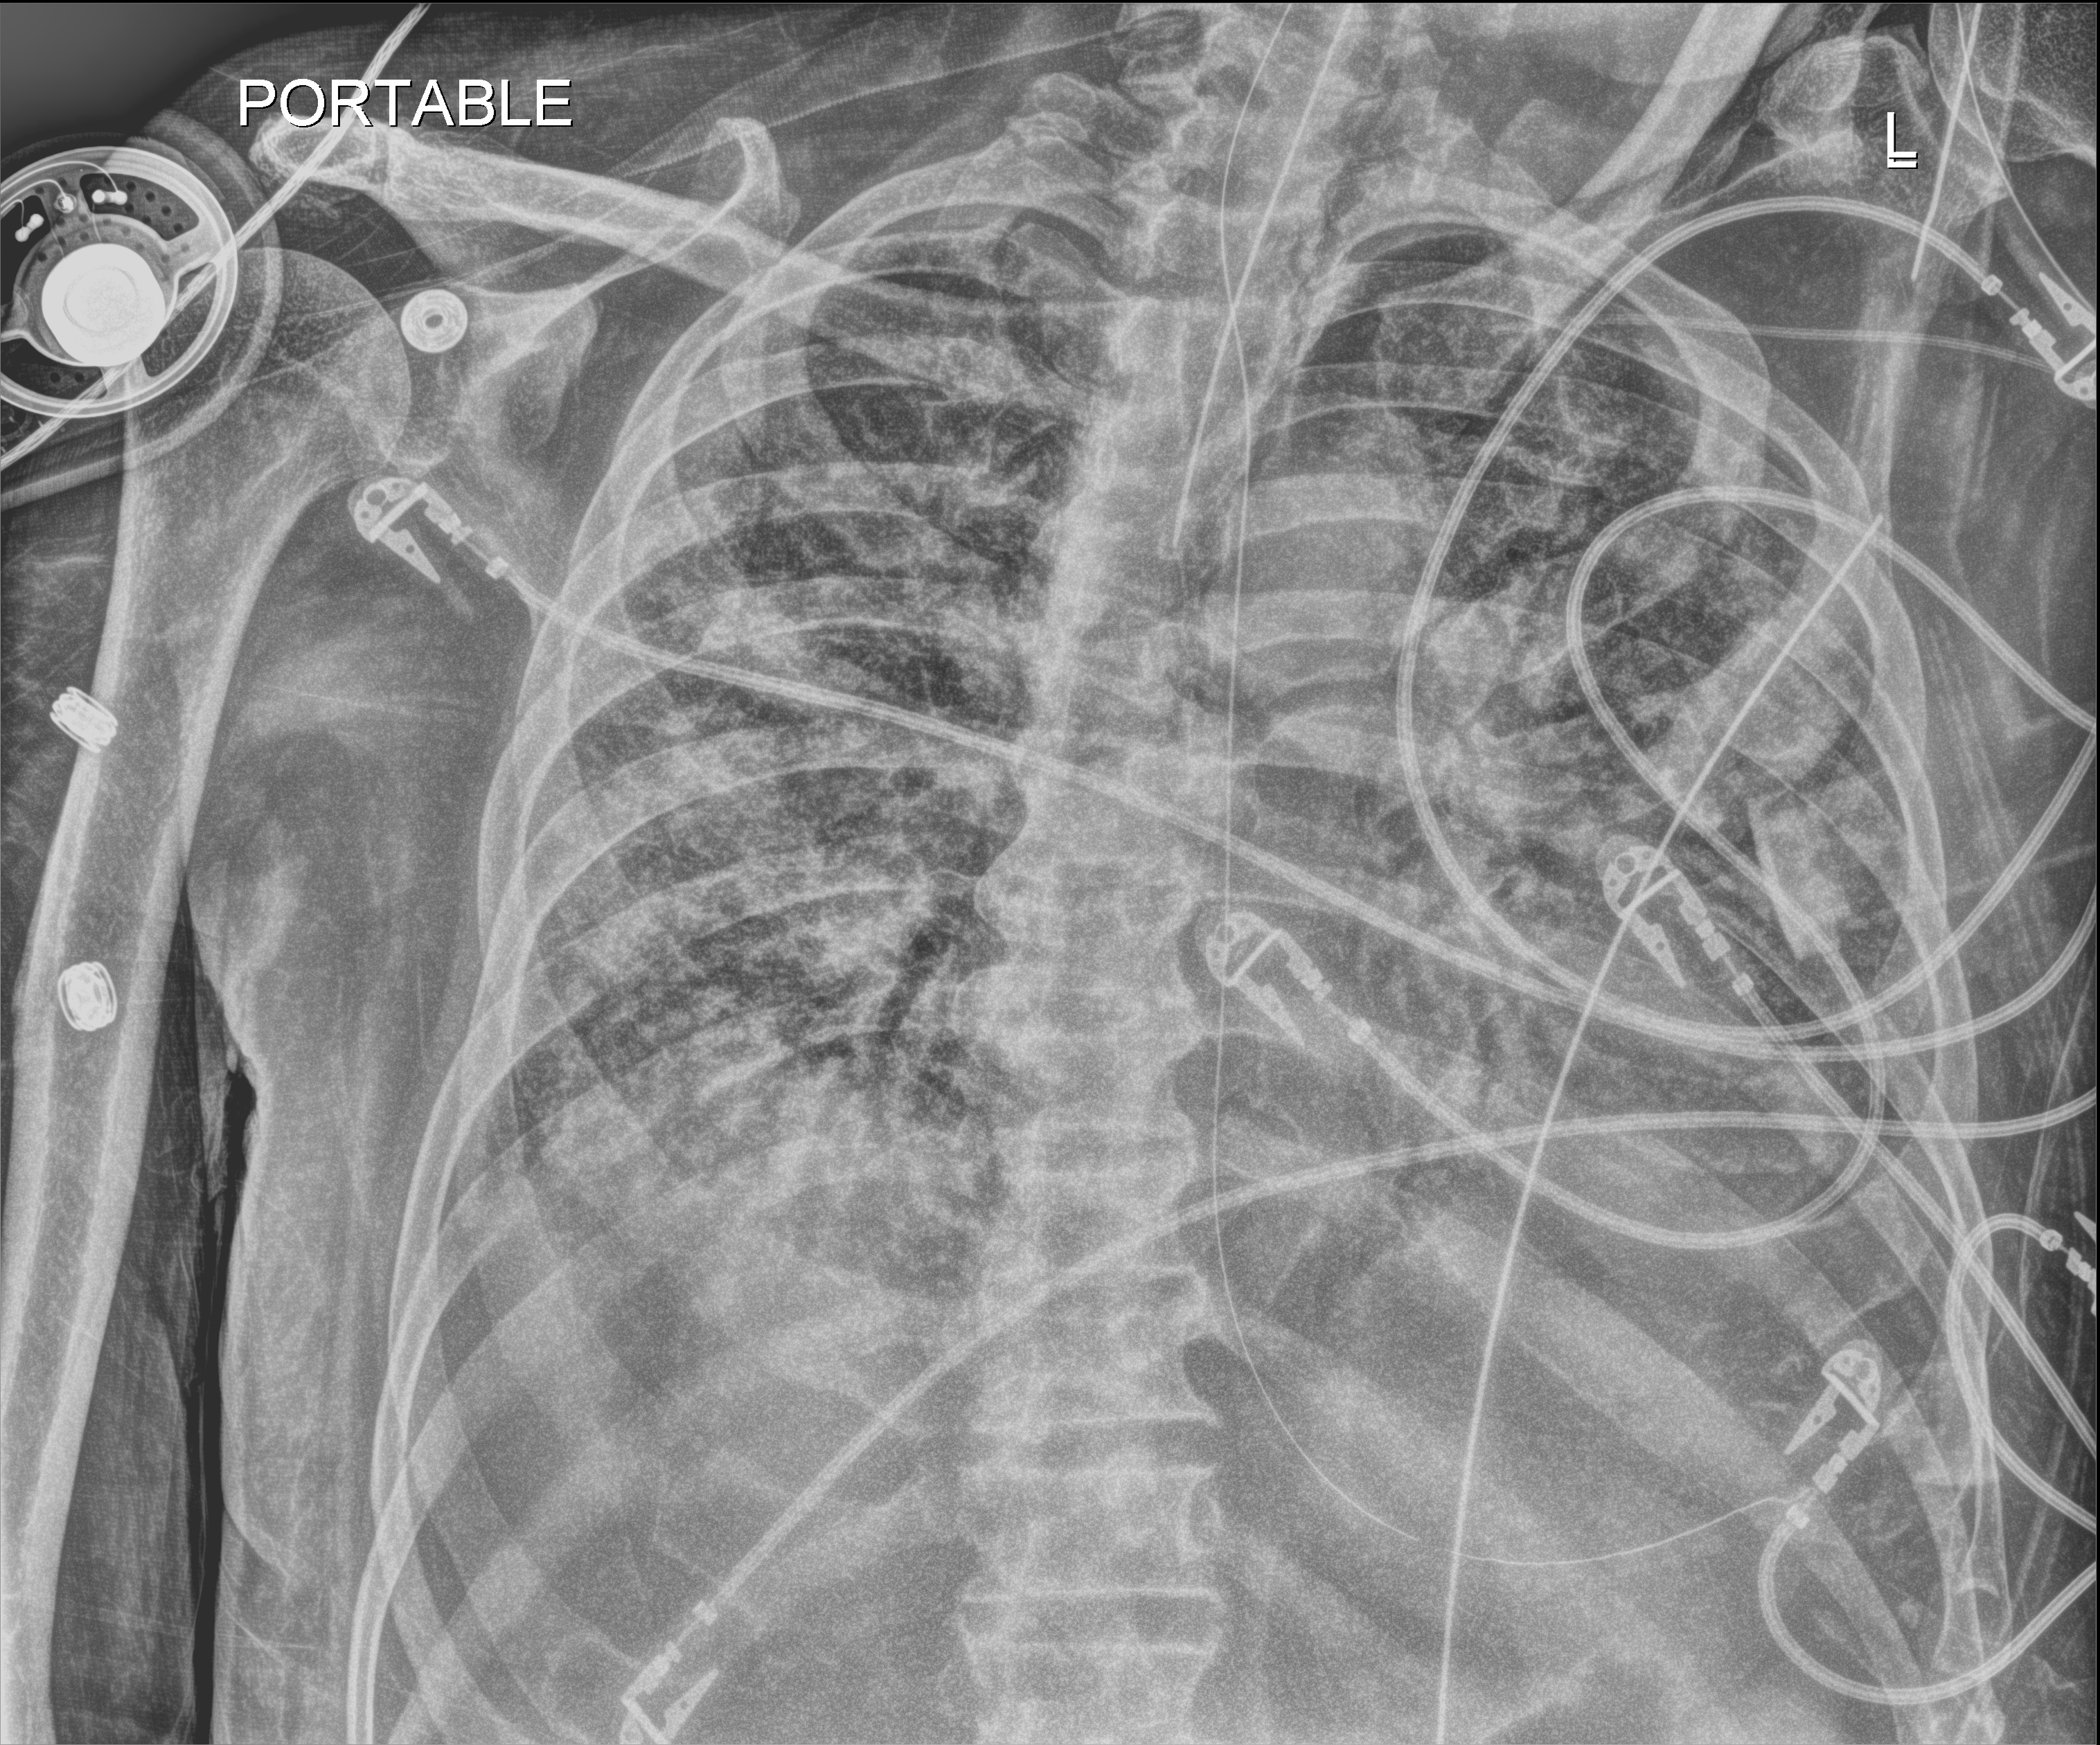
Chest X-ray (portable); anteroposterior (AP) projection. Patient hospitalised with COVID-19; male, aged 75–90 years.
Hospital-stay facts (about this admission, not read from this image; timing relative to this image not recorded): admitted to intensive care during this hospital stay: yes.